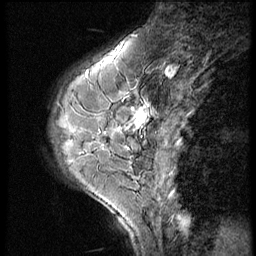
Breast MRI (dynamic contrast-enhanced), one sagittal slice; position 20 of 56 along the scan axis; 3 images stored at this slice position (order not interpretable as contrast timing); 1.5 T; TE 4.2 ms, TR 9 ms; 2.5 mm slice thickness; 256 × 256 image matrix, field of view 180 × 180 mm. Patient: female, 46 years. From the clinical record (not read from this slice): setting: breast cancer imaged before/during neoadjuvant chemotherapy; receptor status: HER2-positive.
Structures marked on this image (semi-automatically segmented with operator editing):
- analysis volume of interest (the breast-tissue region the enhancement analysis was run in; not a lesion): bounding box <73,86,164,161> (left, top, right, bottom; pixels)
- tumour enhancement mask (voxels above the 140 % enhancement threshold inside the analysis volume of interest): <134,108,147,128>